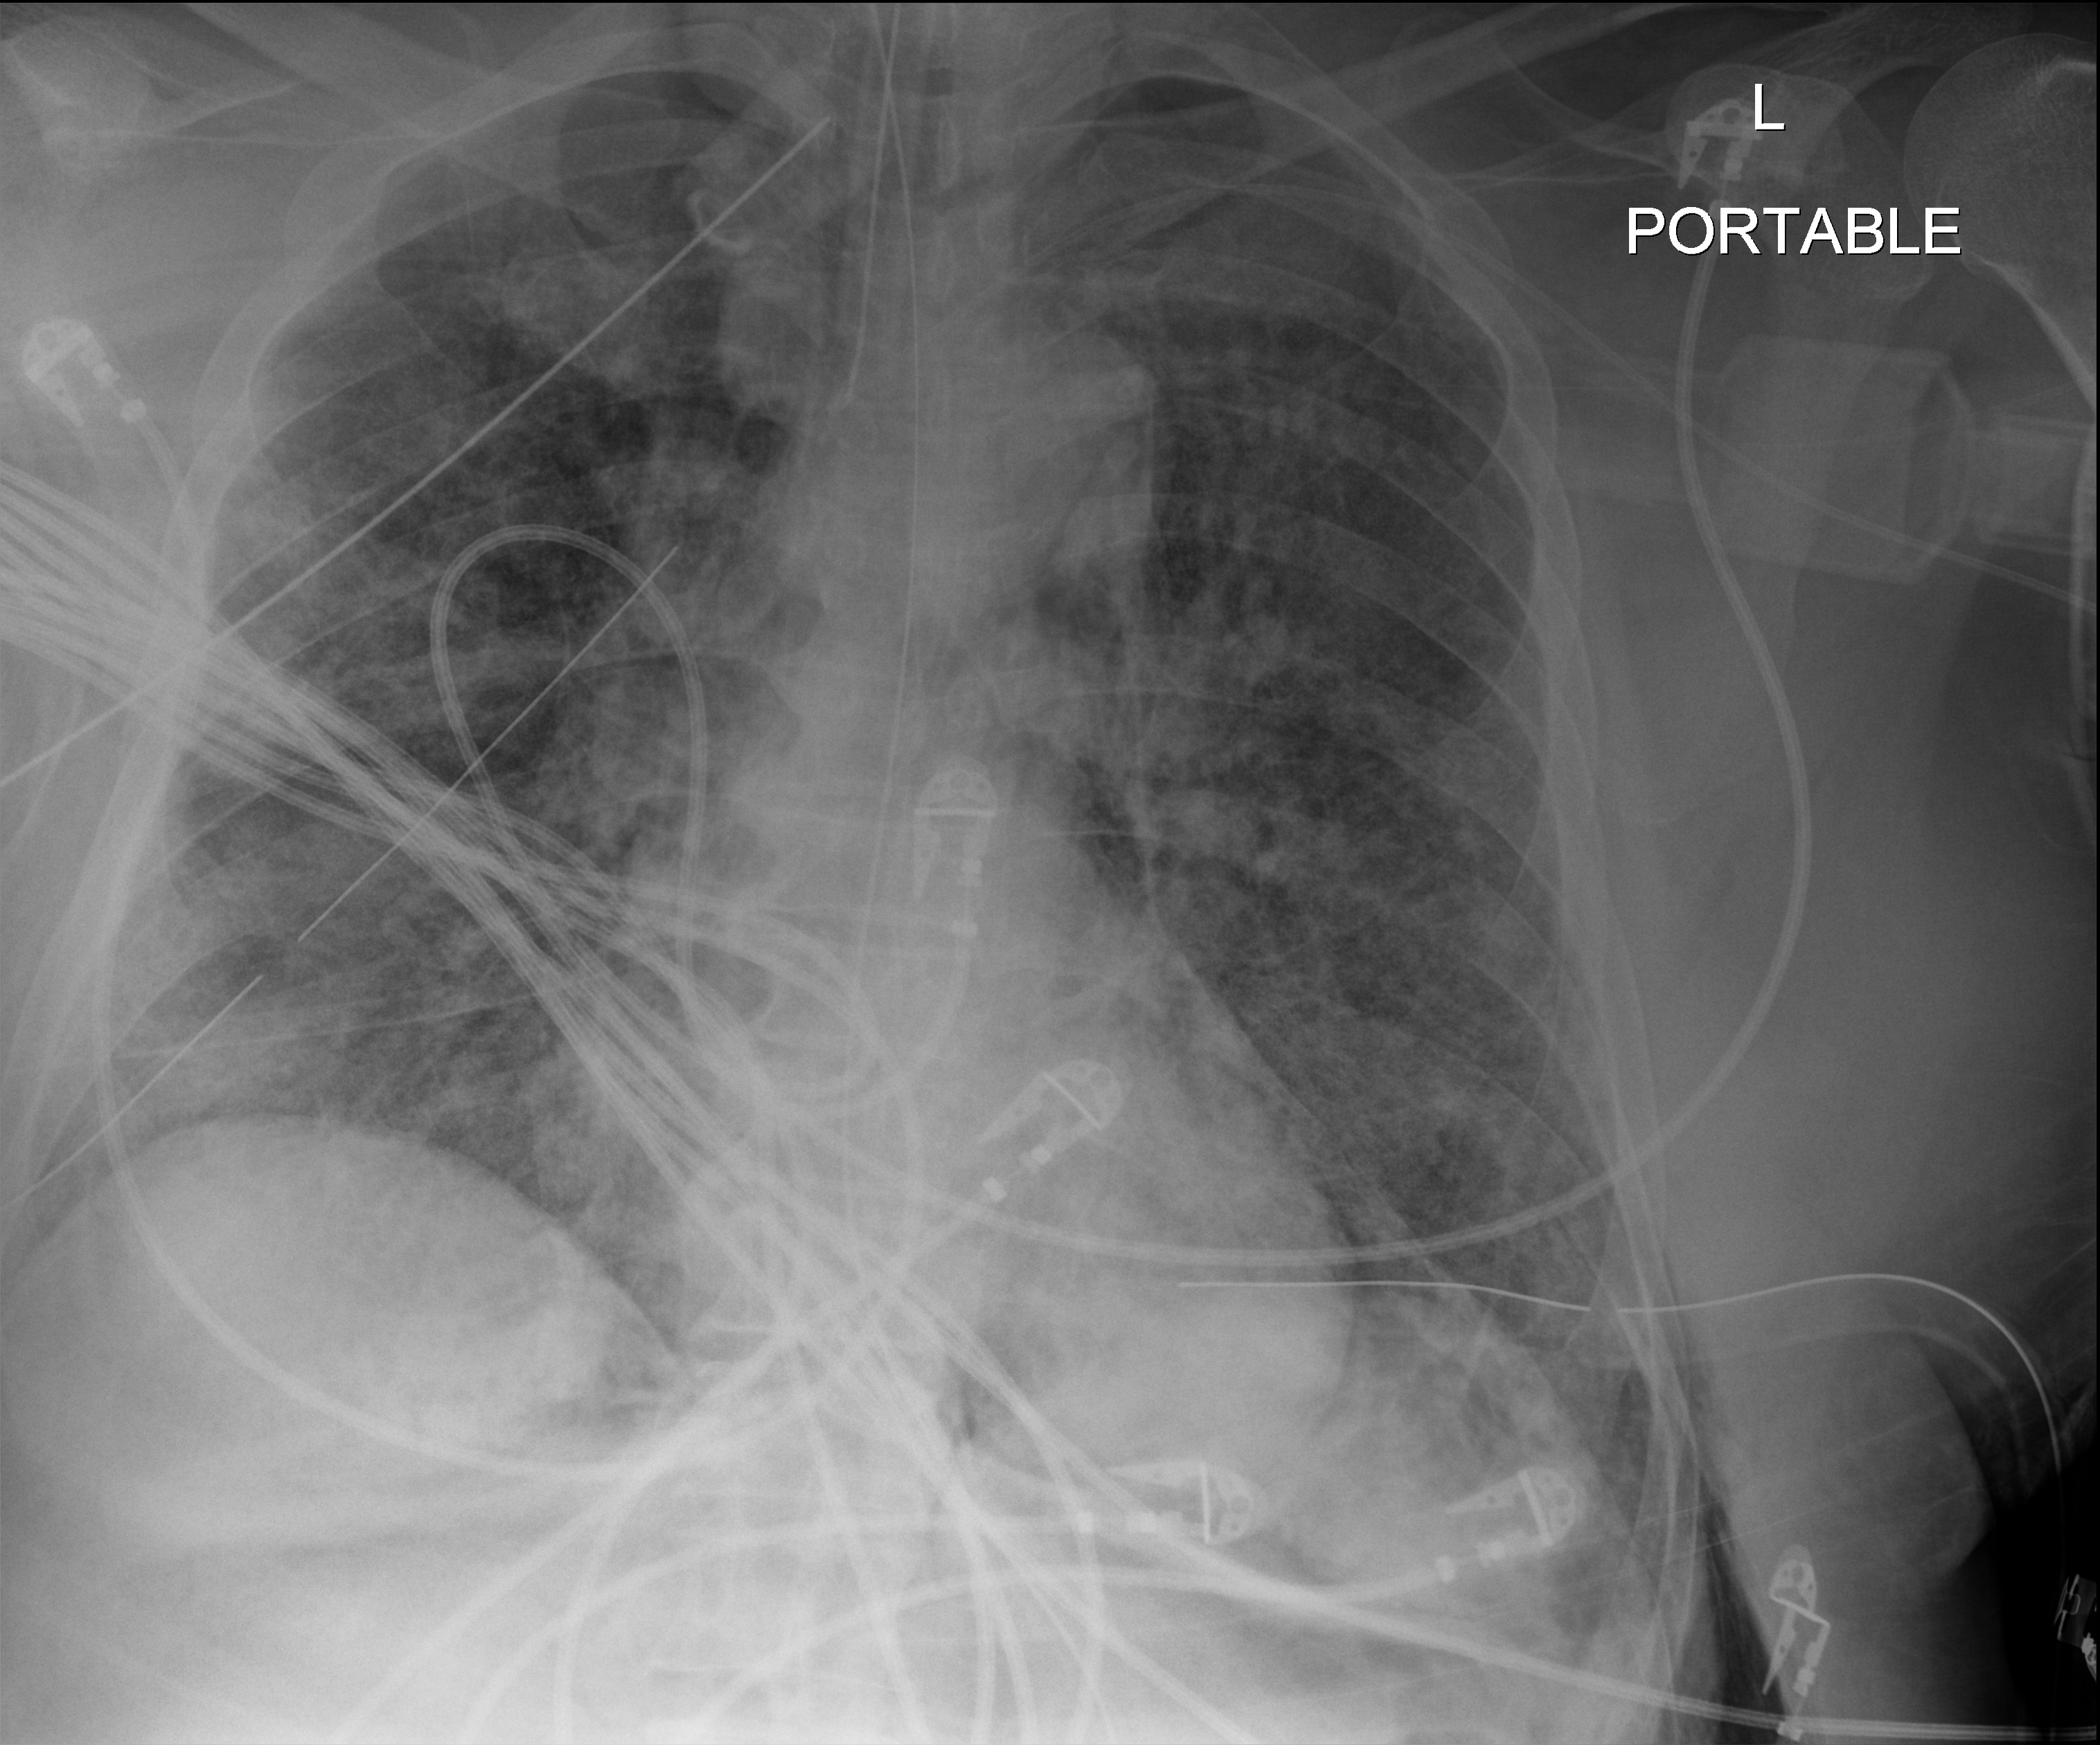
Chest radiograph (digital radiography), anteroposterior (AP) projection. Patient hospitalised with COVID-19, aged 18–59 years.
Admission-level facts for this patient (not findings on this image; timing relative to this image not recorded): admitted to intensive care during this hospital stay: yes; mechanically ventilated during this hospital stay: yes; length of hospital stay: 28 days.